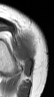
MRI of an extremity soft-tissue mass, one axial slice. Position 17 of 42 along the scan axis. MR volume resampled by the dataset authors to the PET/CT grid (not the native acquisition matrix). 3.27 mm slice thickness. 54 × 97 image matrix, field of view 53 × 95 mm. Female patient. From the clinical record (not read from this slice): histological type: spindle cell suggestive of biphasic synovial sarcoma; grade: intermediate; site of the primary tumour: left knee.
Annotated regions visible in this slice (expert contour drawn on MRI and transferred to this co-registered scan by the dataset authors):
- gross tumour volume including surrounding oedema: bounding box (x1, y1, x2, y2) in pixels: (14, 37, 34, 77)
- gross tumour volume (mass): (14, 41, 34, 77)